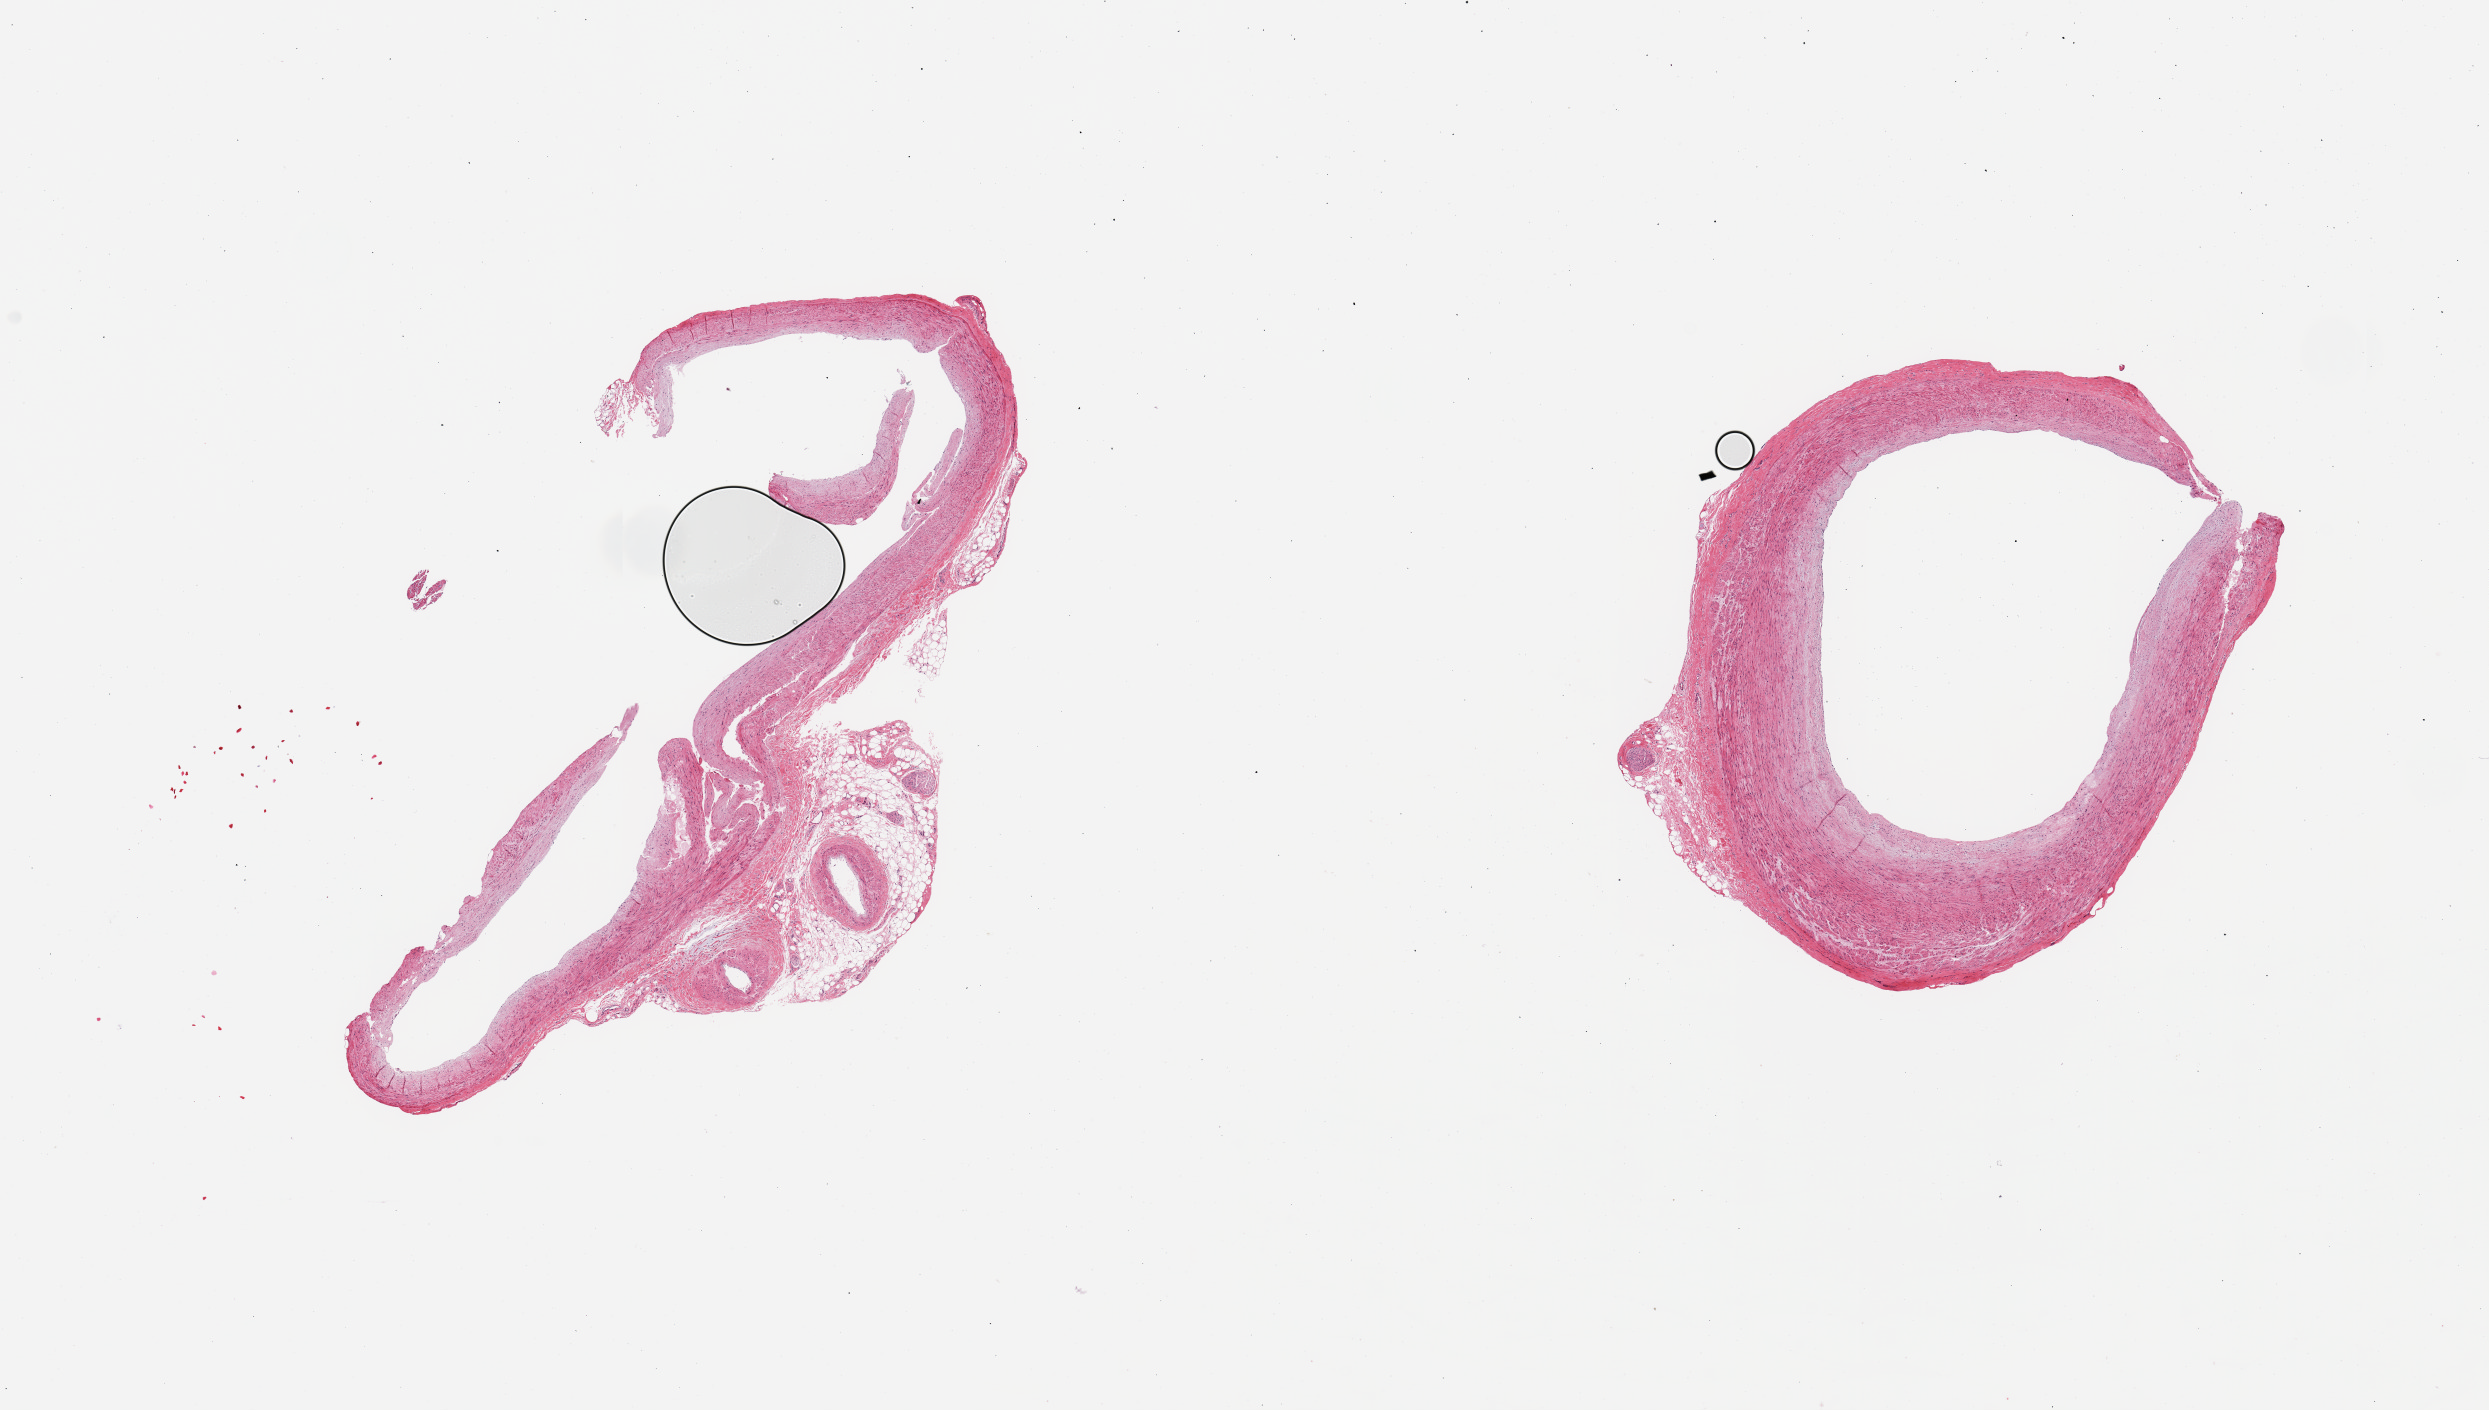
Digitized hematoxylin and eosin (H&E)-stained section, brightfield — whole scanned area (about 19.7 x 11.2 mm) shown as a low-resolution overview. PAXgene-fixed, paraffin-embedded tissue. Target tissue: coronary artery. Donor tissue sample.
Pathologist's review note for this sample: 2 pieces, mild atherosis, ~1.5mm nubbin of adherent fat.